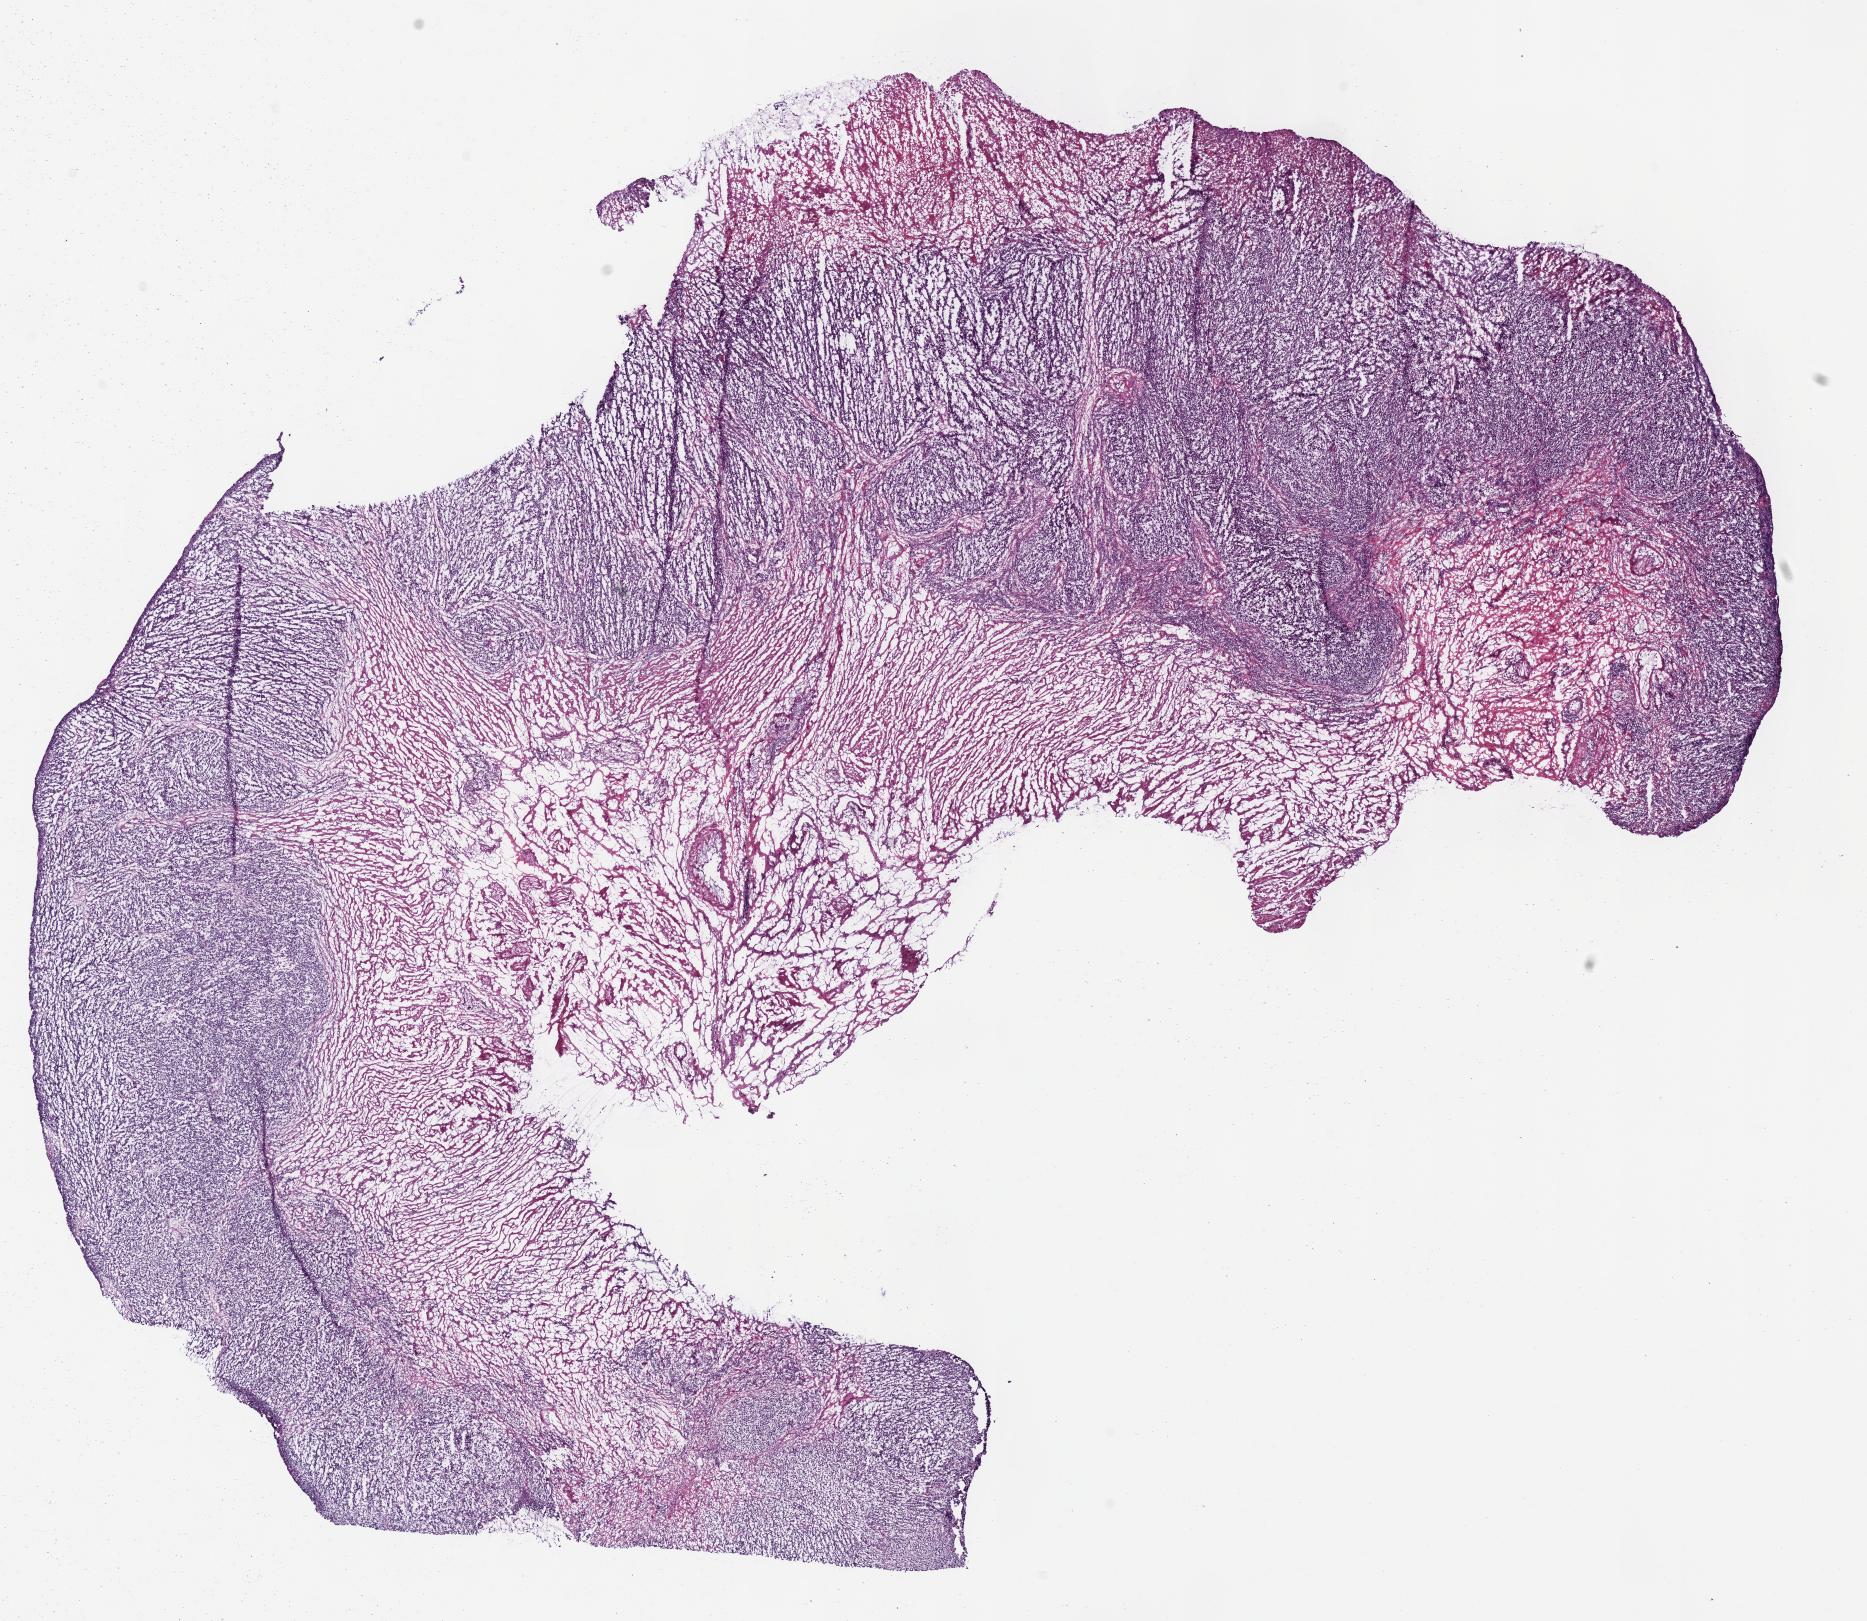
Digitized H&E-stained tissue section (whole slide) — whole scanned area (about 14.7 x 12.7 mm, slide scanned at 40x) shown as a low-resolution overview. Frozen section from the bottom of the tissue portion. Sample: primary tumour, stomach. Female, age 75 years at initial diagnosis. Histologic grade: G3 (poorly differentiated). Slide review estimates, as recorded: tumour cells 70%, tumour nuclei 85%, normal cells 0%, stromal cells 22%, necrosis 8%. Infiltration values recorded for this section: lymphocyte infiltration 4%.
• AJCC pathologic stage: IIB
• histologic diagnosis: Adenocarcinoma, NOS (cardia, NOS)
• lymph nodes positive (case pathology): 4 of 4 examined